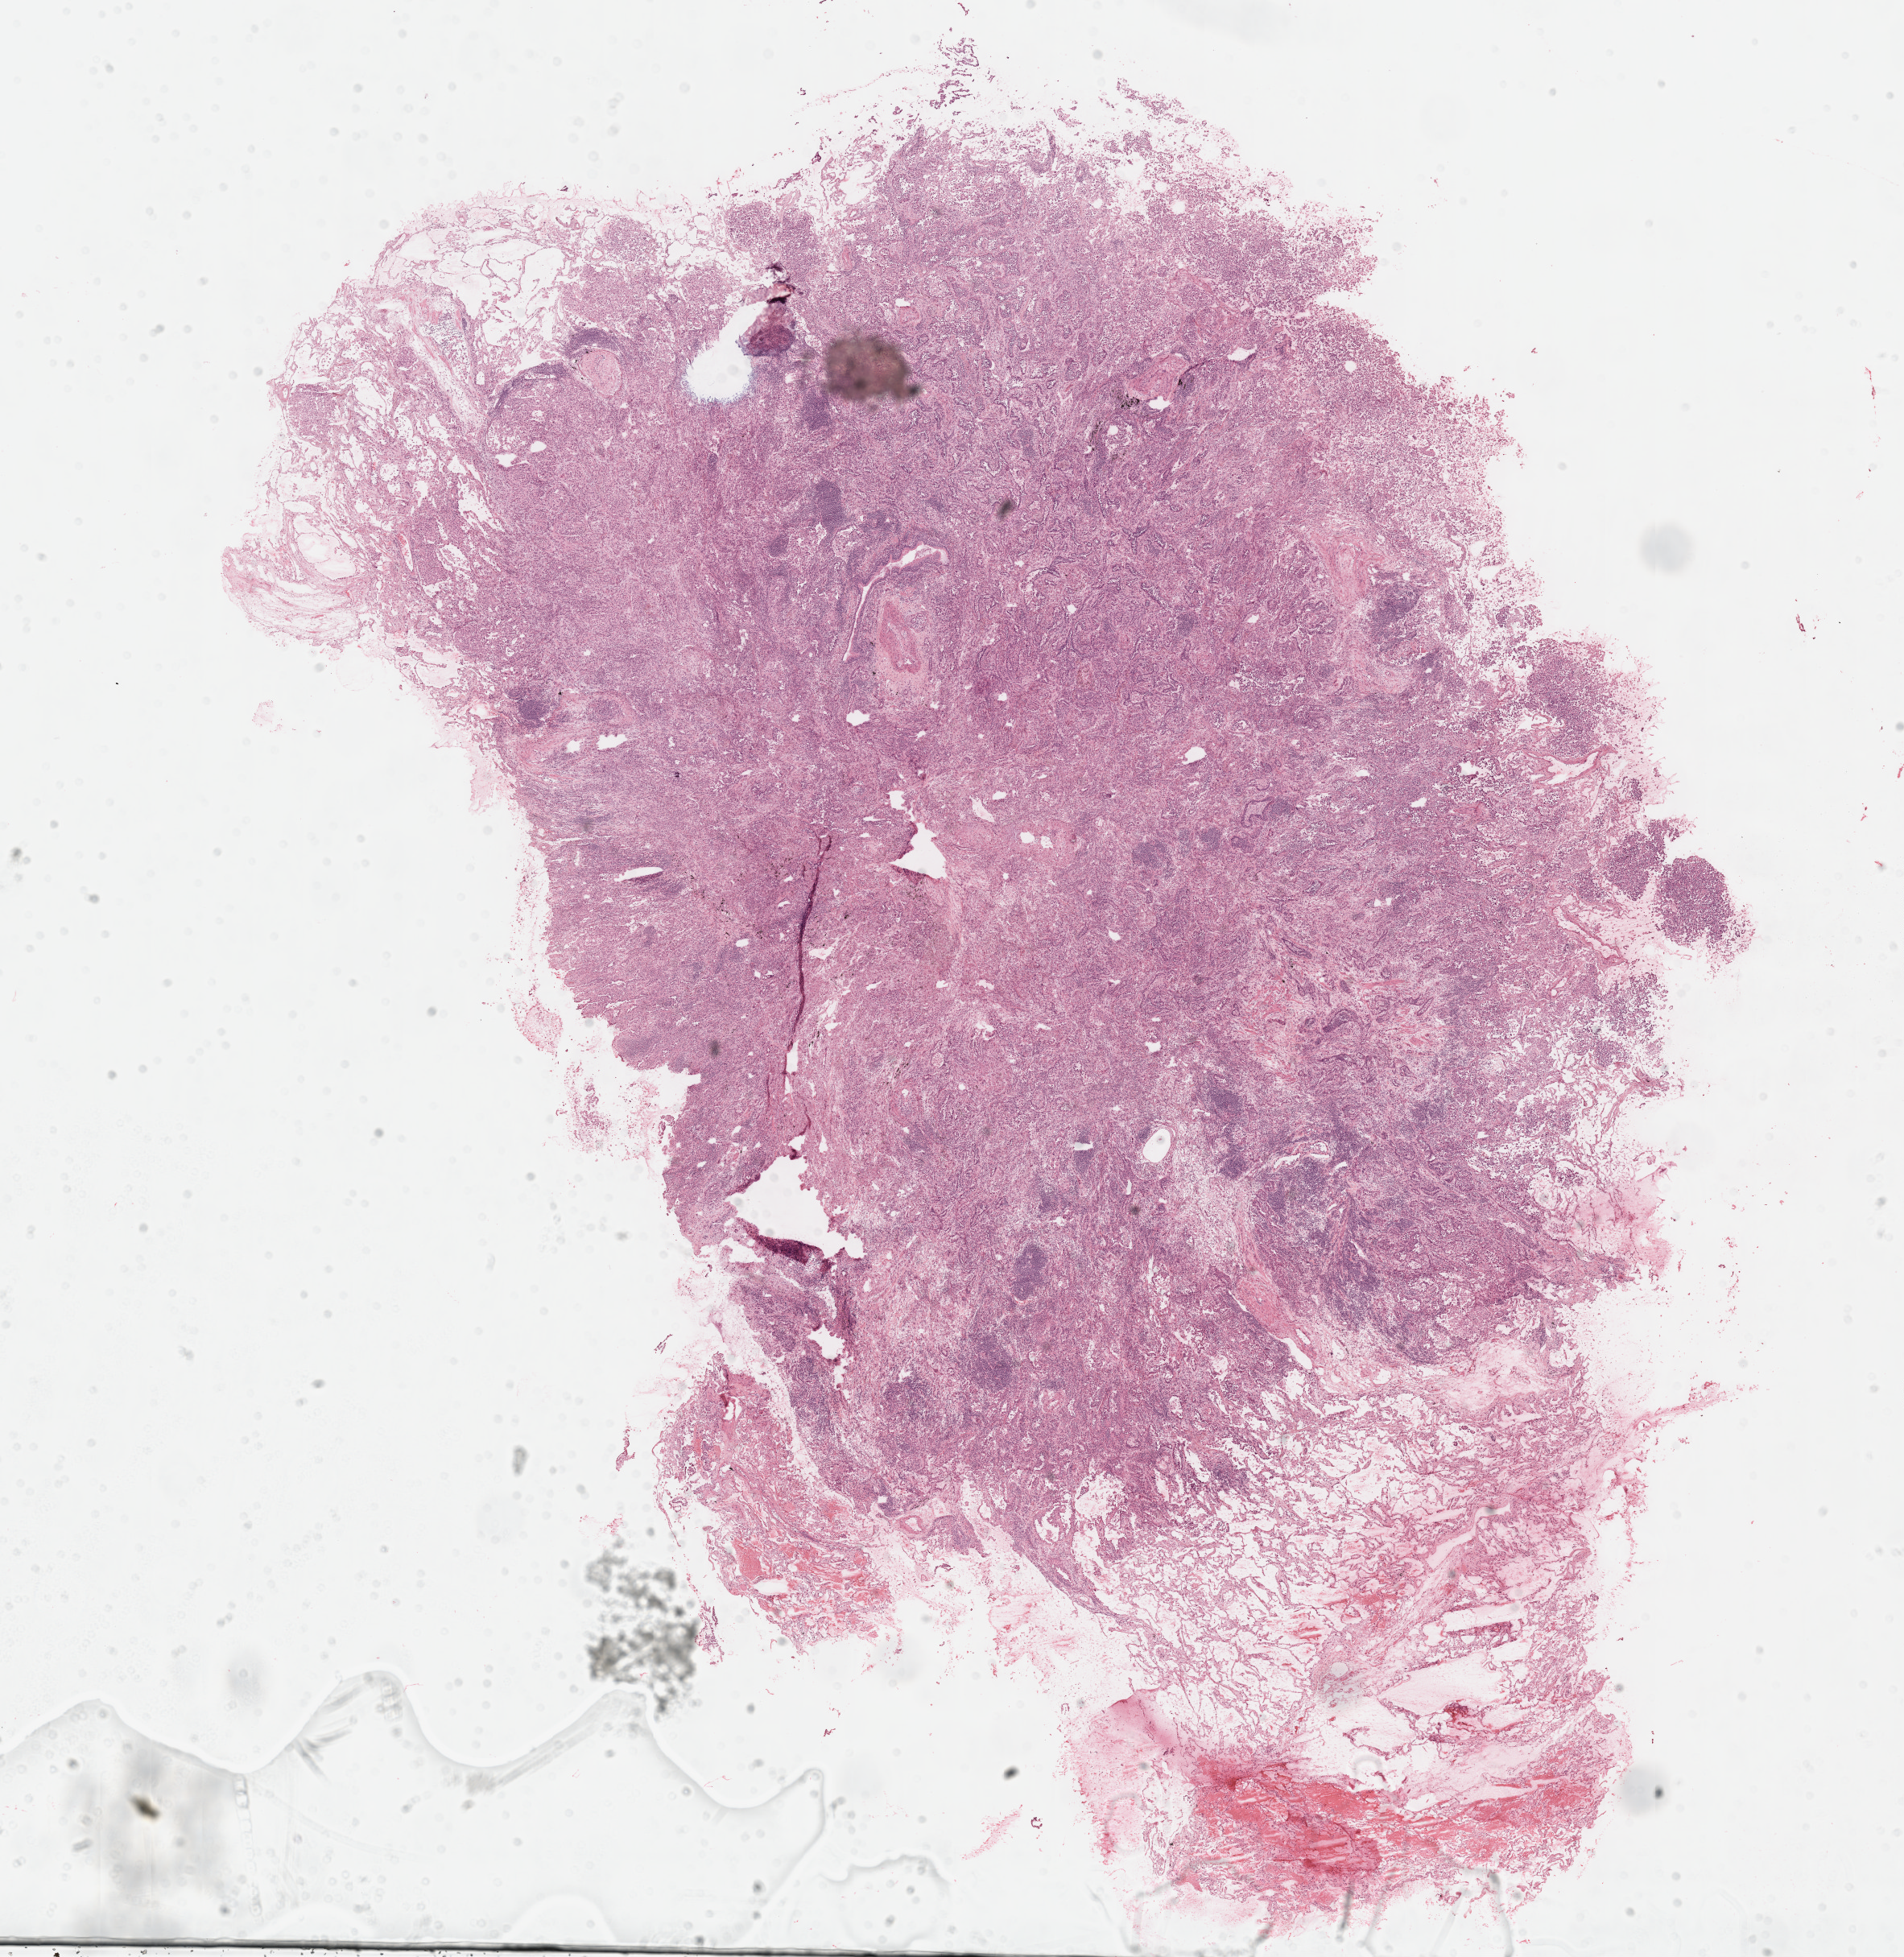
Digitized Hematoxylin and eosin (H&E) stained tissue section (whole slide) — whole scanned area (about 19.1 x 19.7 mm, from a 40x scan) shown as a low-resolution overview, FFPE section, primary tumour sample from the lung. Female patient; age at initial diagnosis 76 years.
* AJCC pathologic stage: IIA (6th edition)
* histologic diagnosis: Adenocarcinoma, NOS (upper lobe, lung)